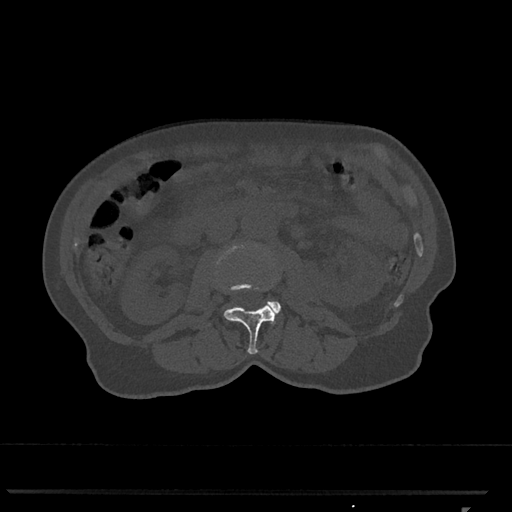
CT including the spine, one axial slice. Position 316 of 793 along the scan axis. Reconstruction kernel Br40s/3. Bone window (W 1800 / L 400 HU). 512 × 512 image matrix, field of view 380 × 380 mm. Patient: female, 62 years. Case-level facts recorded for this patient, not image findings: primary cancer: renal.
Outlined on this slice (semi-automatic segmentation, software-assisted and operator-edited):
- L2 vertebra: bounding box (x1, y1, x2, y2) in pixels: (217, 245, 278, 354)
- L3 vertebra: (258, 289, 281, 313)